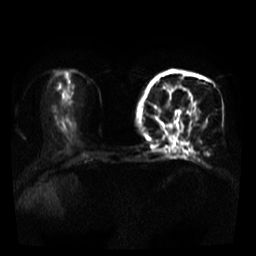
Breast MRI, one axial slice; position 14 of 39 along the scan axis; diffusion-weighted series; image 2 of 4 stored at this slice position (different b-values; order by instance number); 3 T; 5 mm slice thickness; 256 × 256 image matrix, field of view 320 × 320 mm. Female patient.
Outlined on this slice (manually delineated by an expert):
- tumour on diffusion-weighted imaging: bounding box (x1, y1, x2, y2) in pixels: (176, 84, 183, 88)